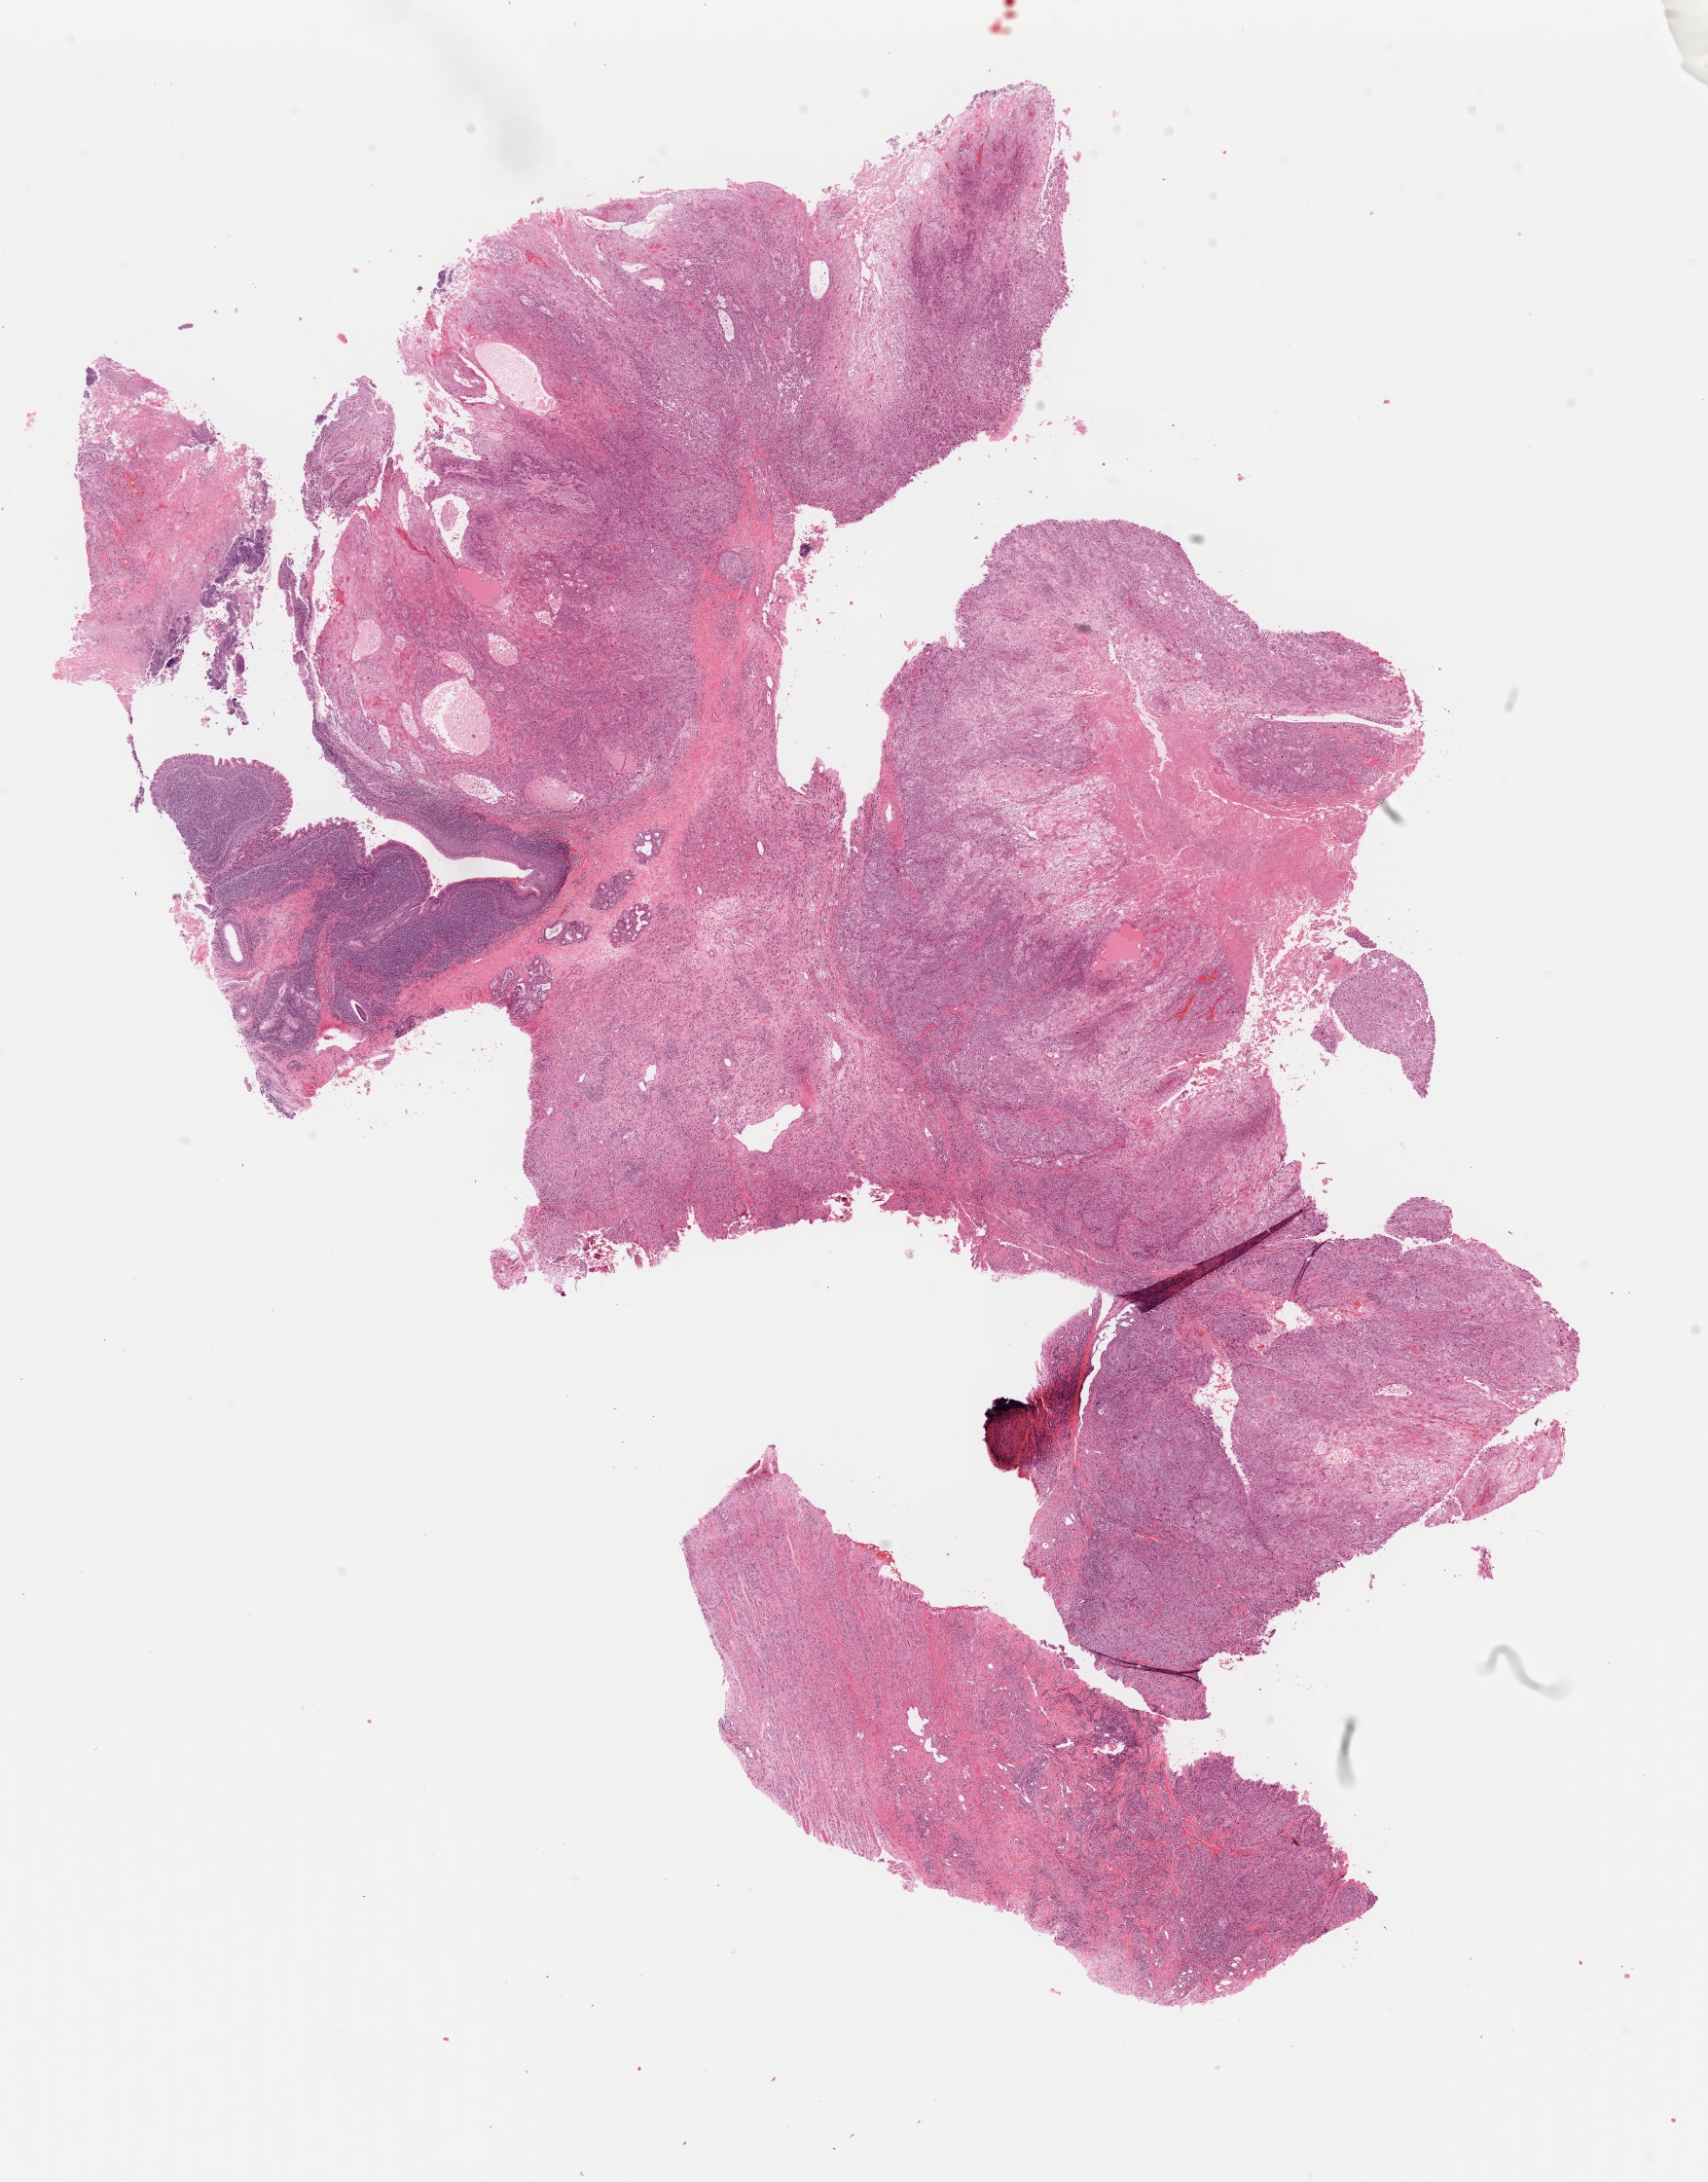
Digitized H&E-stained tissue section (whole slide) — whole scanned area (about 13.9 x 17.7 mm, slide scanned at 40x) shown as a low-resolution overview. Formalin-fixed paraffin-embedded (FFPE) diagnostic section. Primary tumour sample from the head and neck. Patient: male, age at initial diagnosis 75 years. Histologic grade: G1 (well differentiated).
• histologic diagnosis: Squamous cell carcinoma, keratinizing, NOS (larynx, NOS)
• AJCC pathologic stage: III (7th edition)
• TNM: T3 NX M0